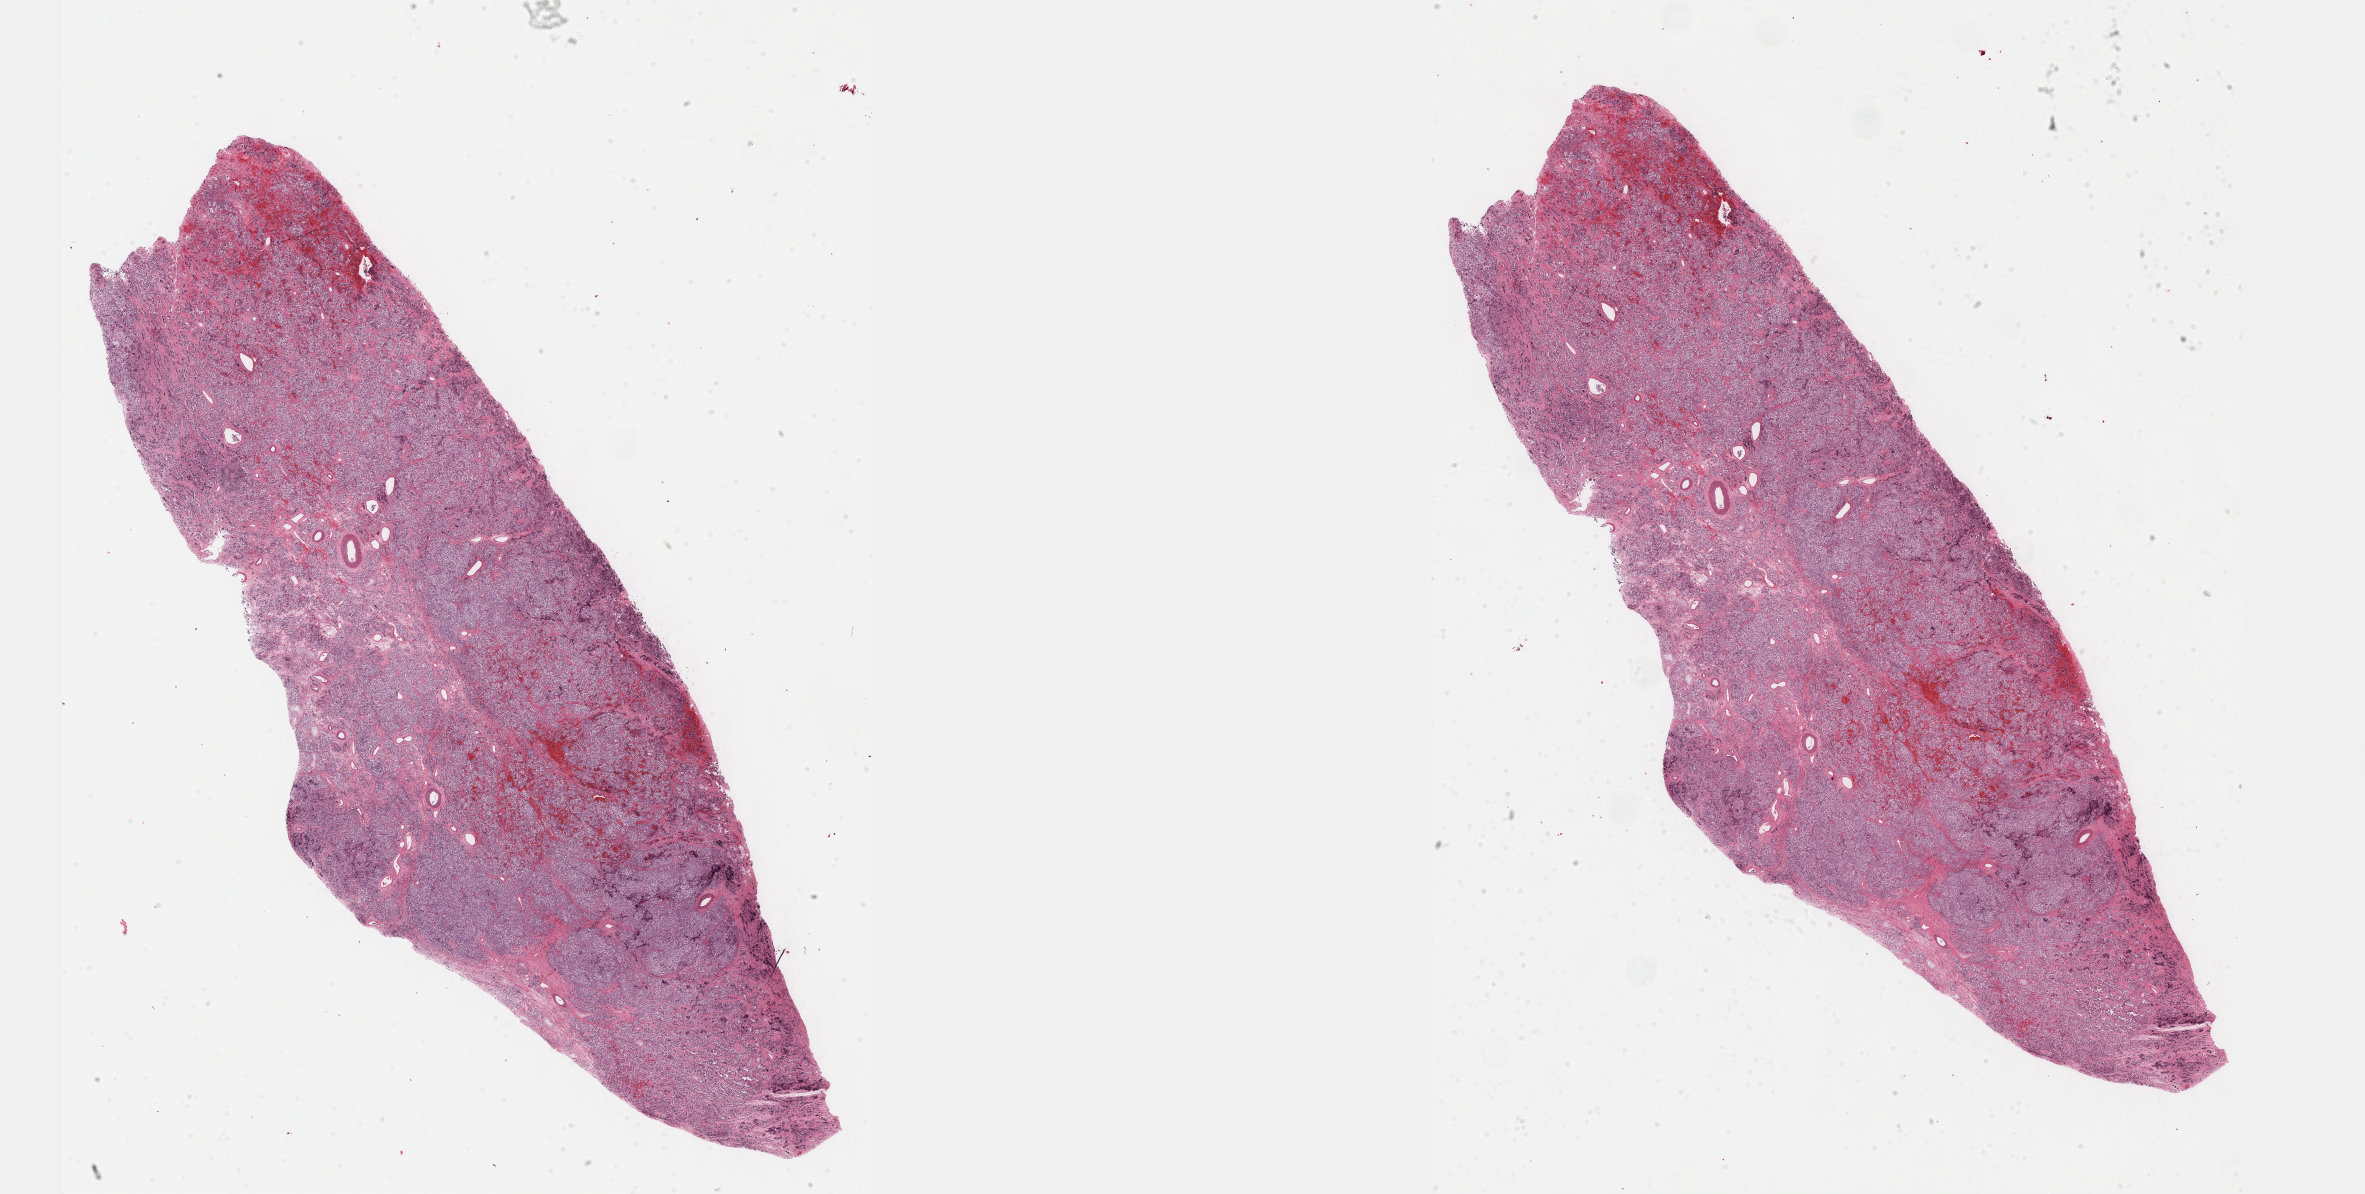
Digitized Hematoxylin and eosin (H&E) stained tissue section (whole slide), low-resolution overview of the scanned area, about 38.2 x 19.3 mm; formalin-fixed paraffin-embedded (FFPE) diagnostic section; testis, primary tumour sample. Male, age 29 years at initial diagnosis.
Pathologic diagnosis: Seminoma, NOS.